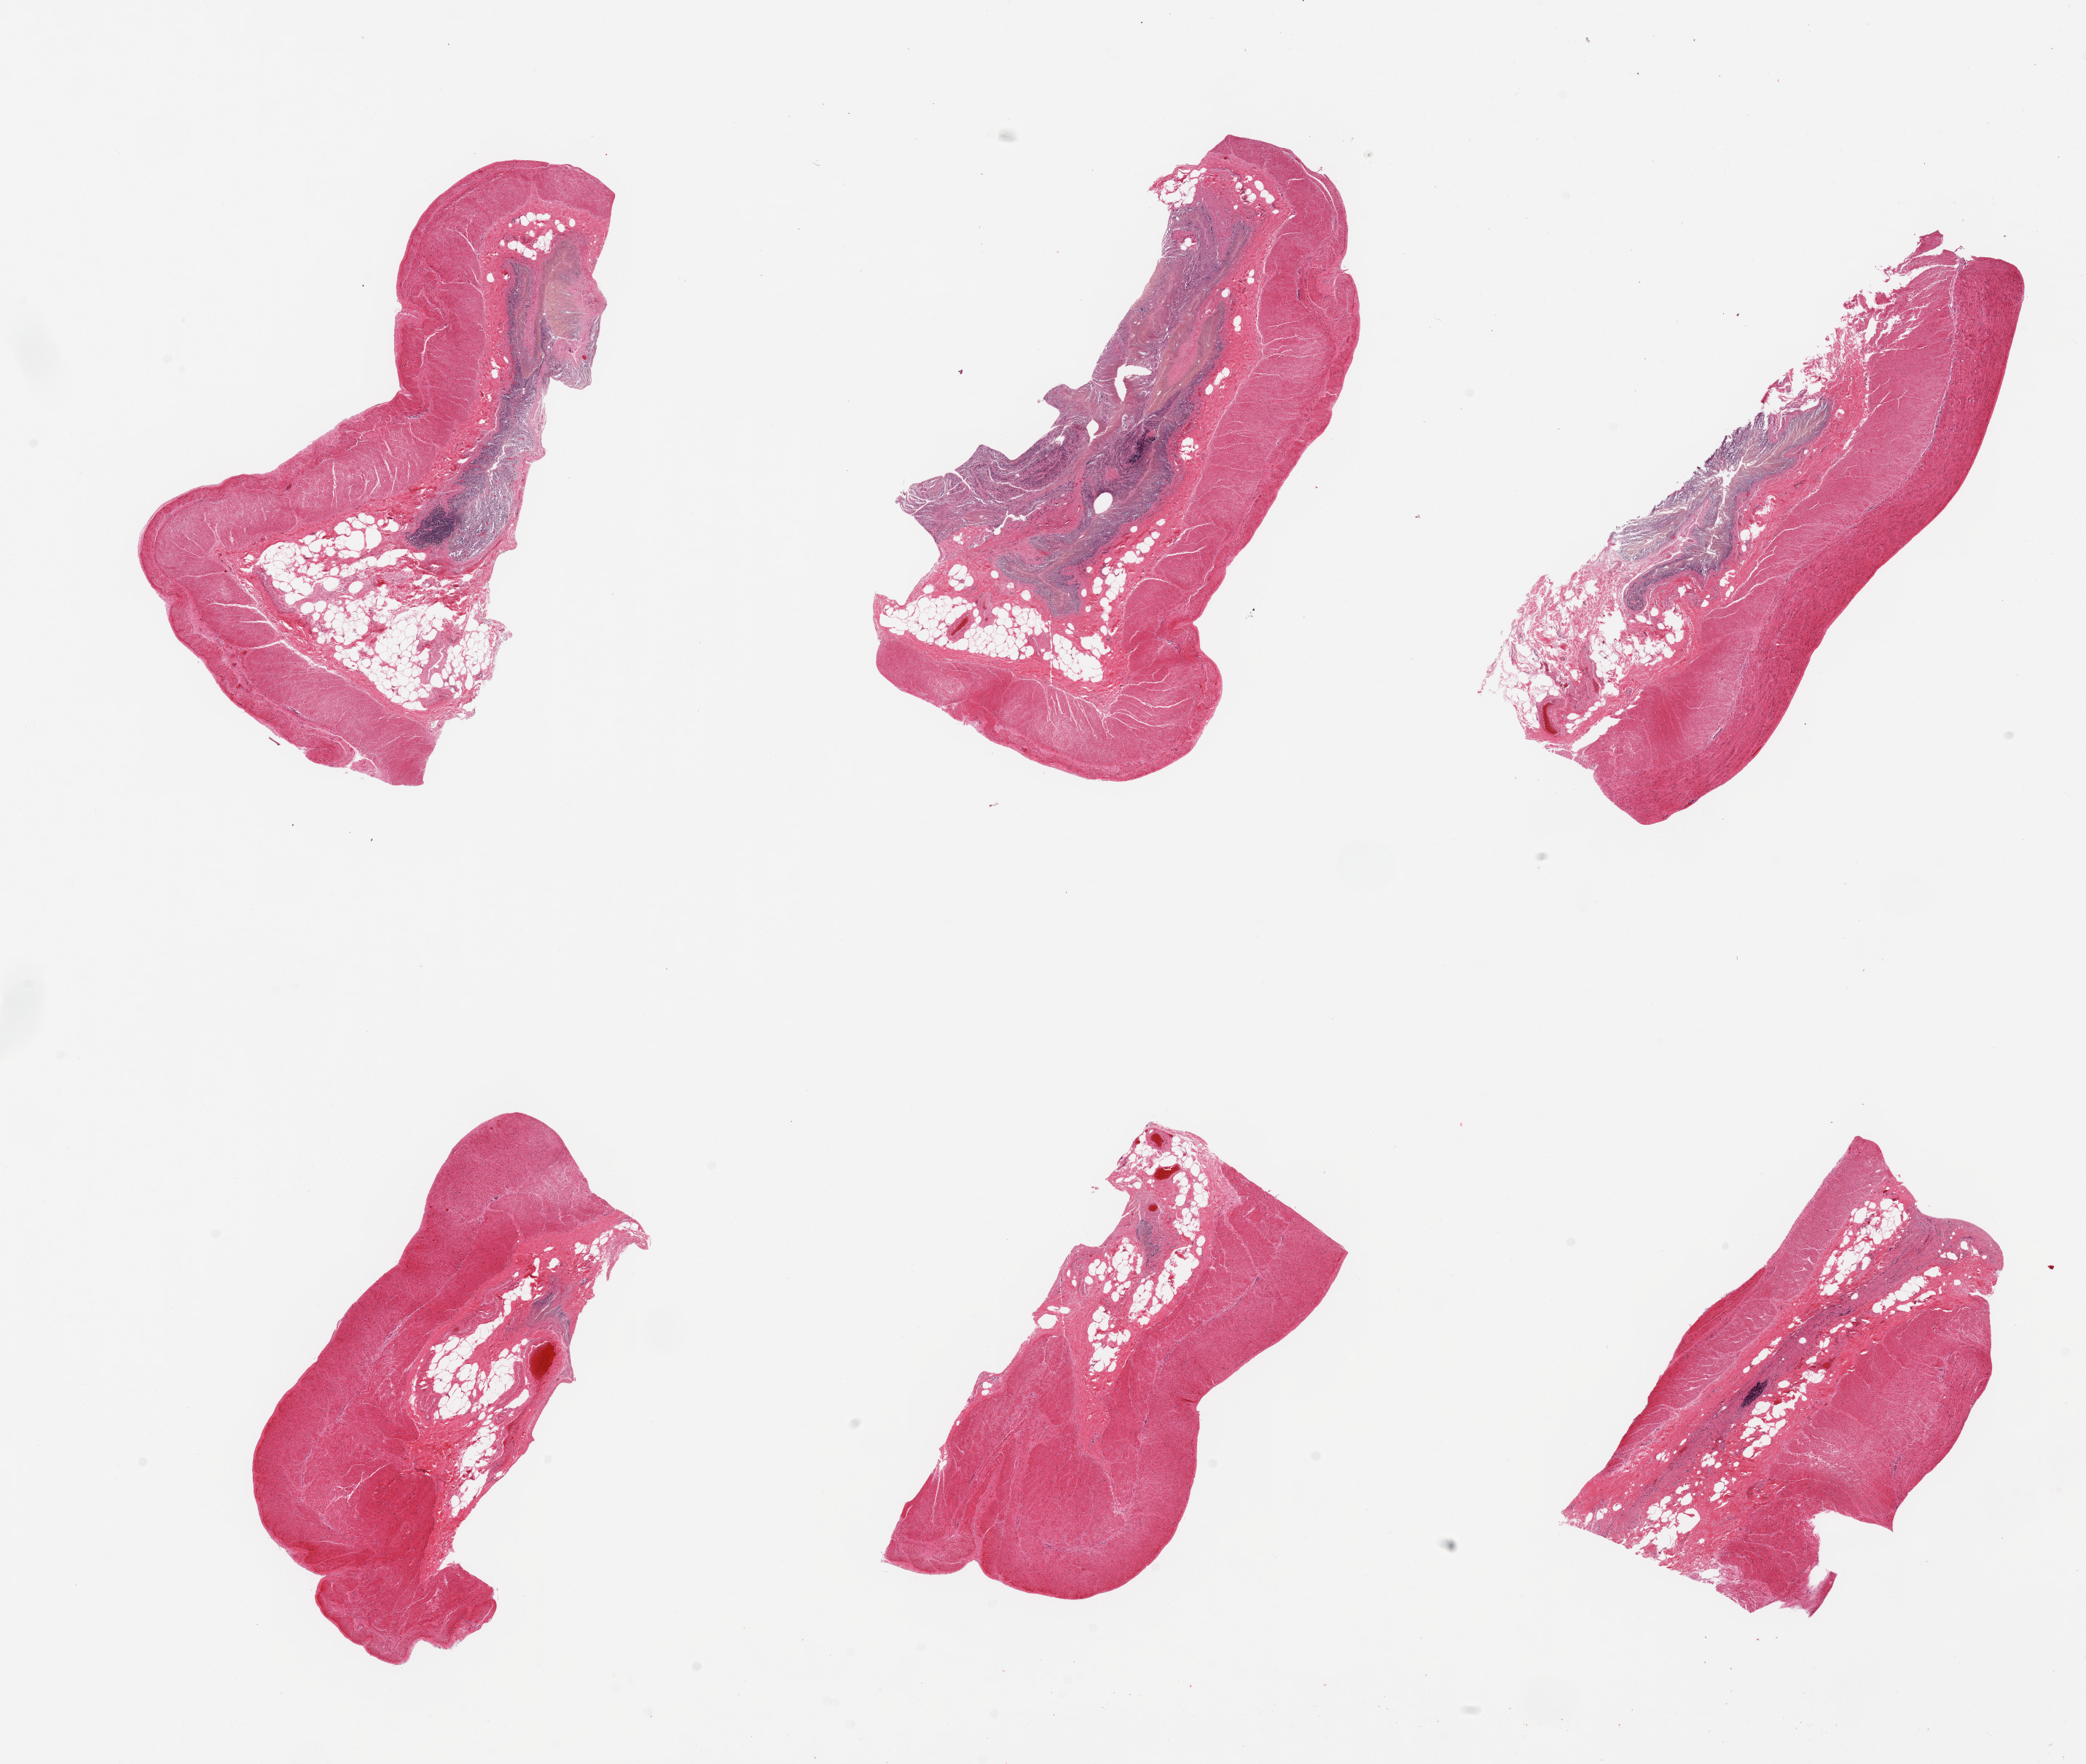
Digitized haematoxylin and eosin-stained section, brightfield — low-resolution overview of the scanned area, about 22.6 x 19.1 mm (from a 20x scan), PAXgene-fixed paraffin-embedded (PFPE) section, target tissue: transverse colon, donor tissue sample. Donor sex: male.
Review note (as recorded): 6 pieces, target mucosa up to ~0.6mm, advanced autolysis.